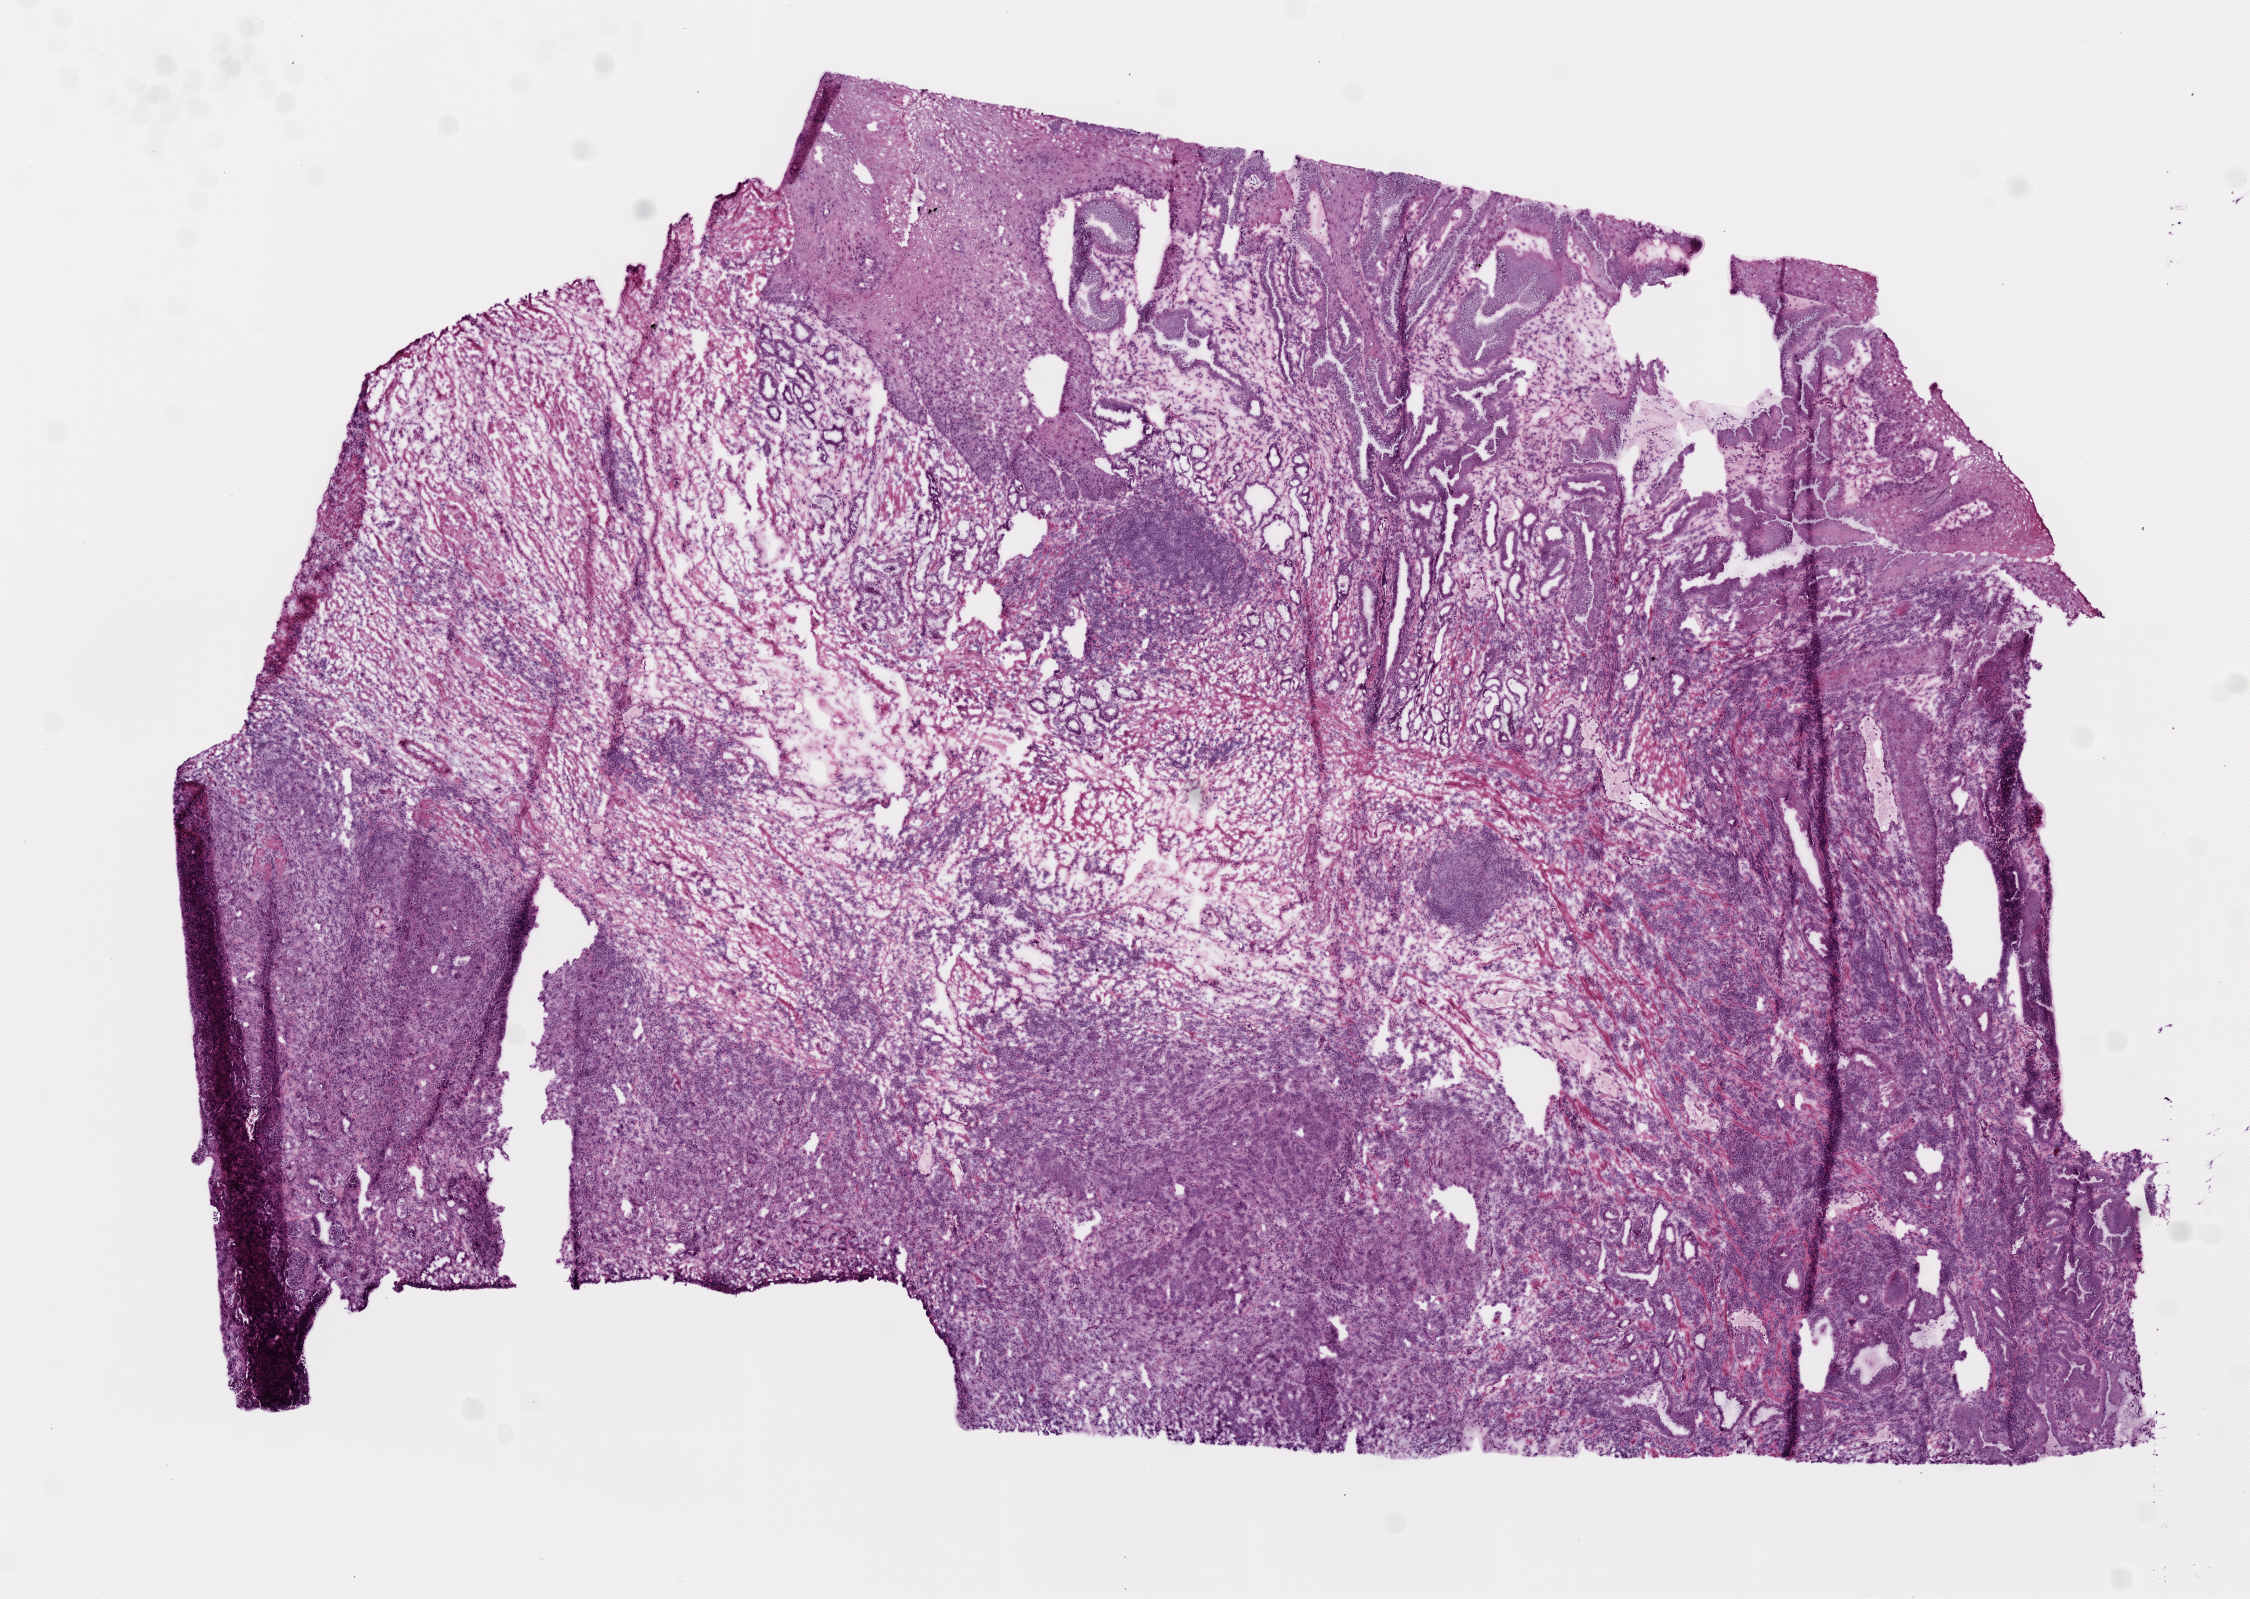
H&E whole-slide image, low-resolution overview of the scanned area, about 9.0 x 6.4 mm (slide scanned at 20x); frozen section from the top of the tissue portion; primary tumour sample from the stomach. Patient: female, age at initial diagnosis 58 years. Slide review estimates, as recorded: tumour cells 72%, tumour nuclei 75%.
Histologic diagnosis: Adenocarcinoma, intestinal type (cardia, NOS).